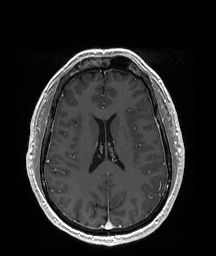
Brain MRI from a brain-tumour surgery series, one axial slice; position 84 of 192 along the scan axis; T1-weighted post-contrast; 1 mm slice thickness; 216 × 256 image matrix, field of view 219 × 260 mm. From the clinical record (not read from this slice): histopathology: Glioblastoma; WHO grade: 4; IDH mutation: no.
Annotated regions visible in this slice (manually delineated by an expert):
- tumour: bounding box [x1, y1, x2, y2] px = [141, 178, 165, 210]